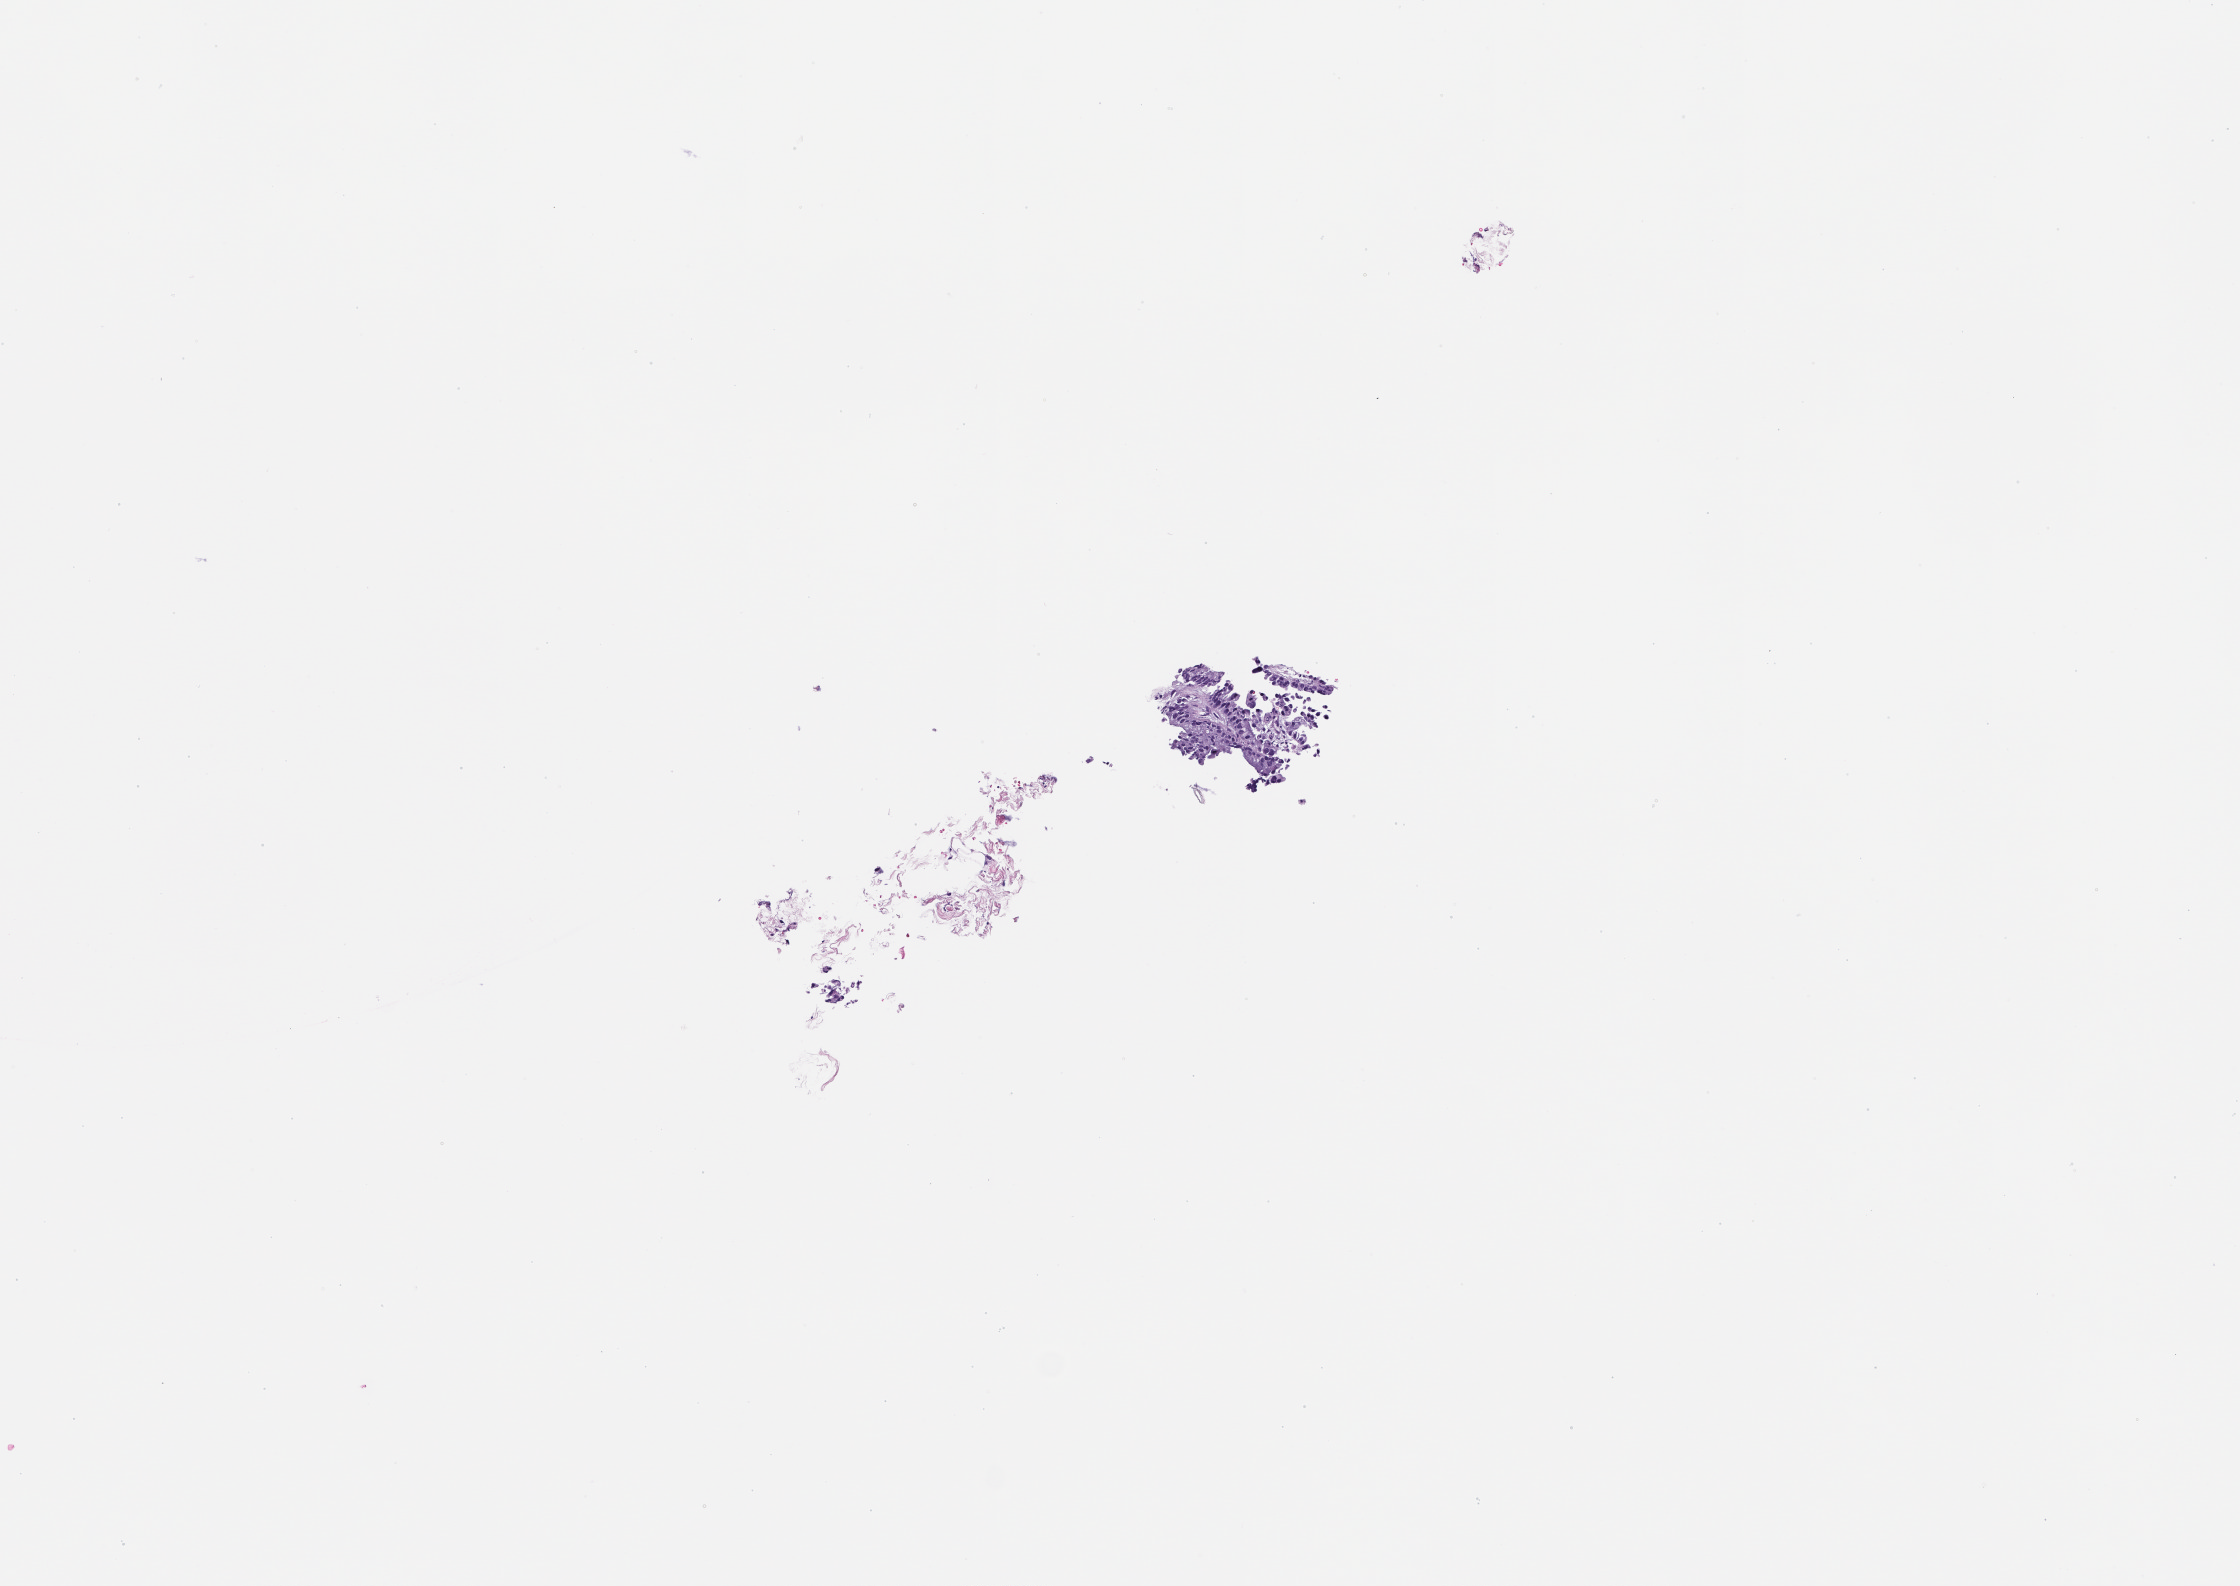
Whole-slide image, haematoxylin and eosin stain, shown as a low-resolution overview of the whole scanned area (about 4.5 x 3.2 mm); formalin-fixed paraffin-embedded section; archival tissue. Male patient.
- this section: metastatic tumor tissue
- primary diagnosis of the patient: Non-Small Cell Lung Carcinoma